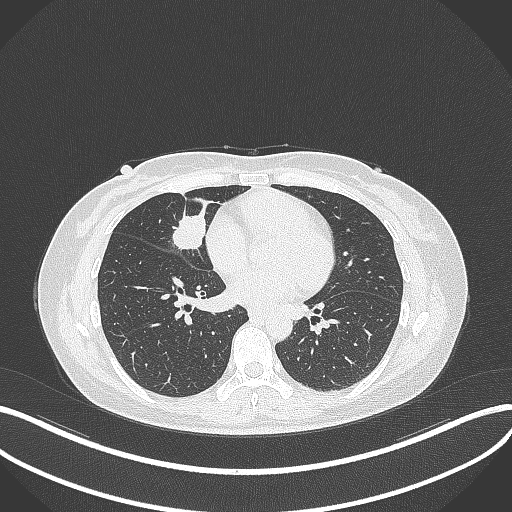
Chest CT, one axial slice; slice 125 of 284 in the series (ordered by position); 120 kVp; lung window (W 1500 / L -600 HU); 1 mm slice thickness; 512 × 512 image matrix, field of view 400 × 400 mm. Female patient, age 43 years. From the clinical record (not read from this slice): clinical TNM (as recorded): T1c N3 M1; histopathological grade: G1.
Structures marked on this image (bounding box drawn by a radiologist):
- lung tumour (recorded histology: adenocarcinoma): box from (x=167, y=201) to (x=208, y=256) px